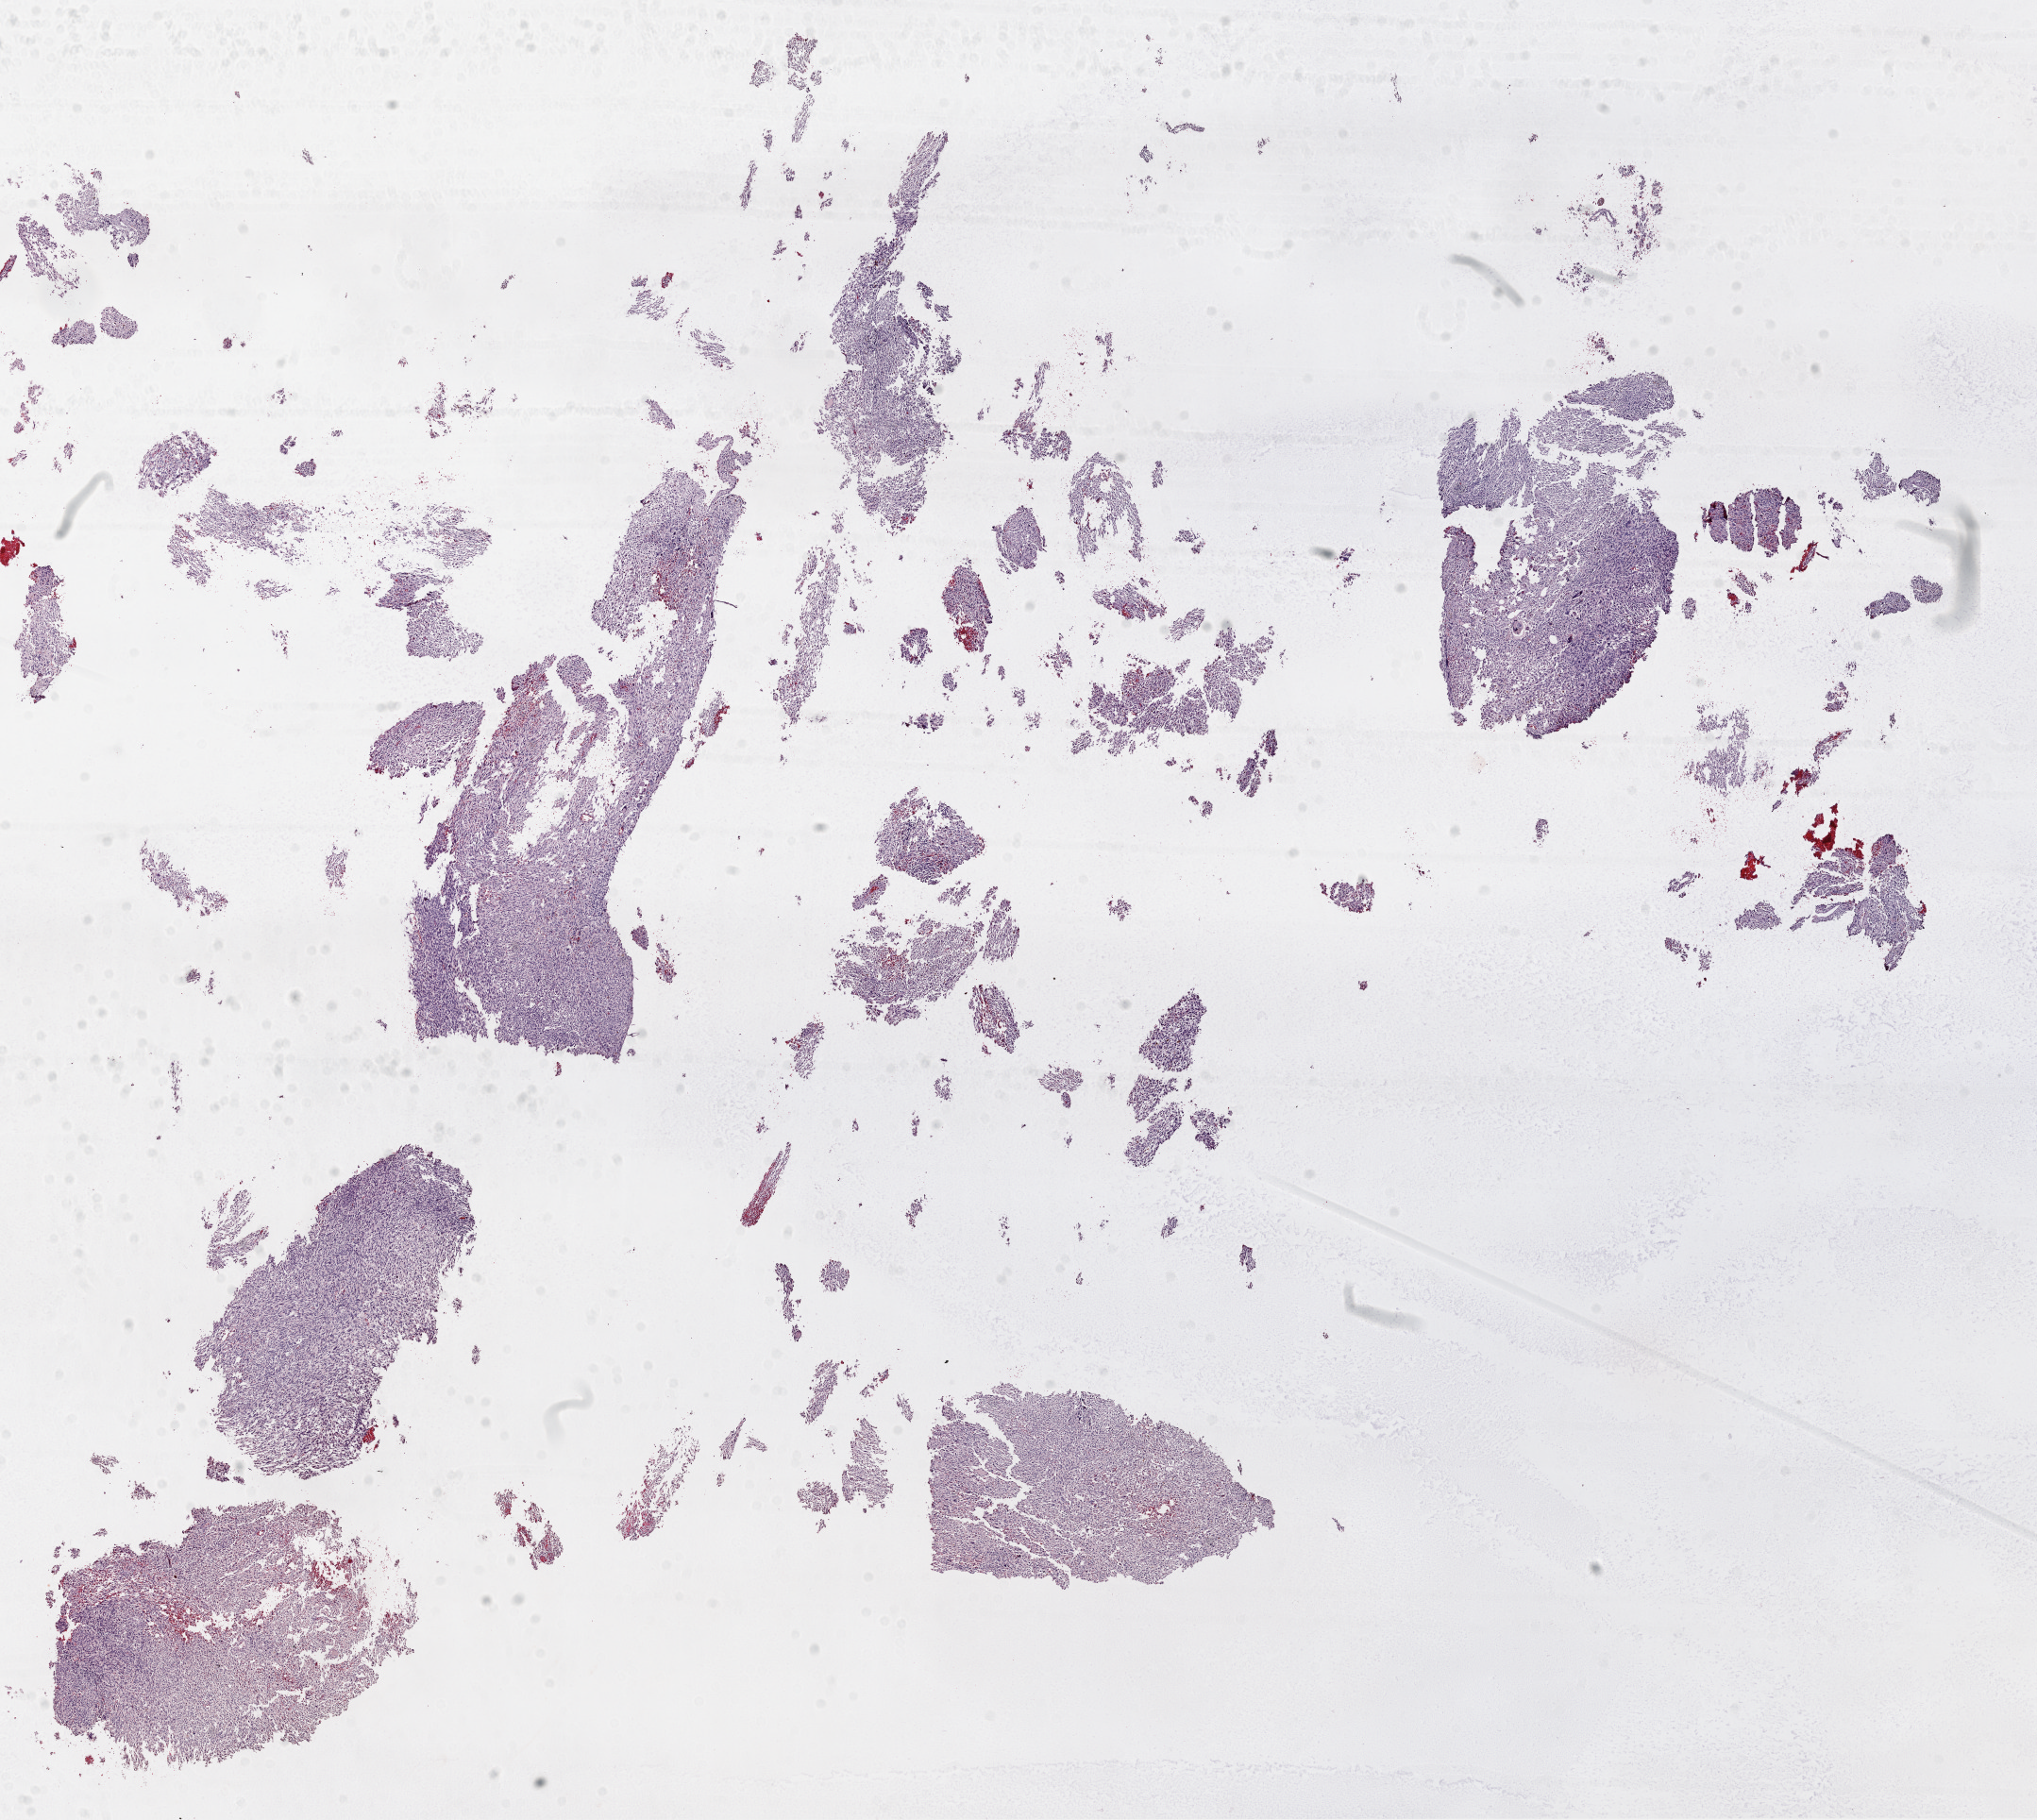
H&E whole-slide image — a low-resolution overview of the entire scanned area, about 17.4 x 15.6 mm, FFPE section, brain, primary tumour sample. Female patient; age at initial diagnosis 74 years.
- pathologic diagnosis: Glioblastoma